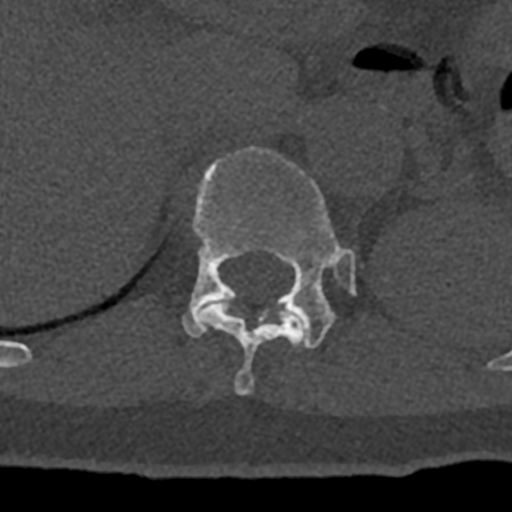
CT including the spine, one axial slice; slice 515 of 797 in the series (ordered by position); bone window (W 1800 / L 400 HU); 0.5 mm slice thickness; 512 × 512 image matrix, field of view 160 × 160 mm. Patient: male, 74 years. From the clinical record (not read from this slice): primary cancer: renal.
Outlined on this slice (semi-automatically segmented with operator editing):
- T11 vertebra: bounding box <197,301,305,395> (left, top, right, bottom; pixels)
- T12 vertebra: <183,146,356,349>